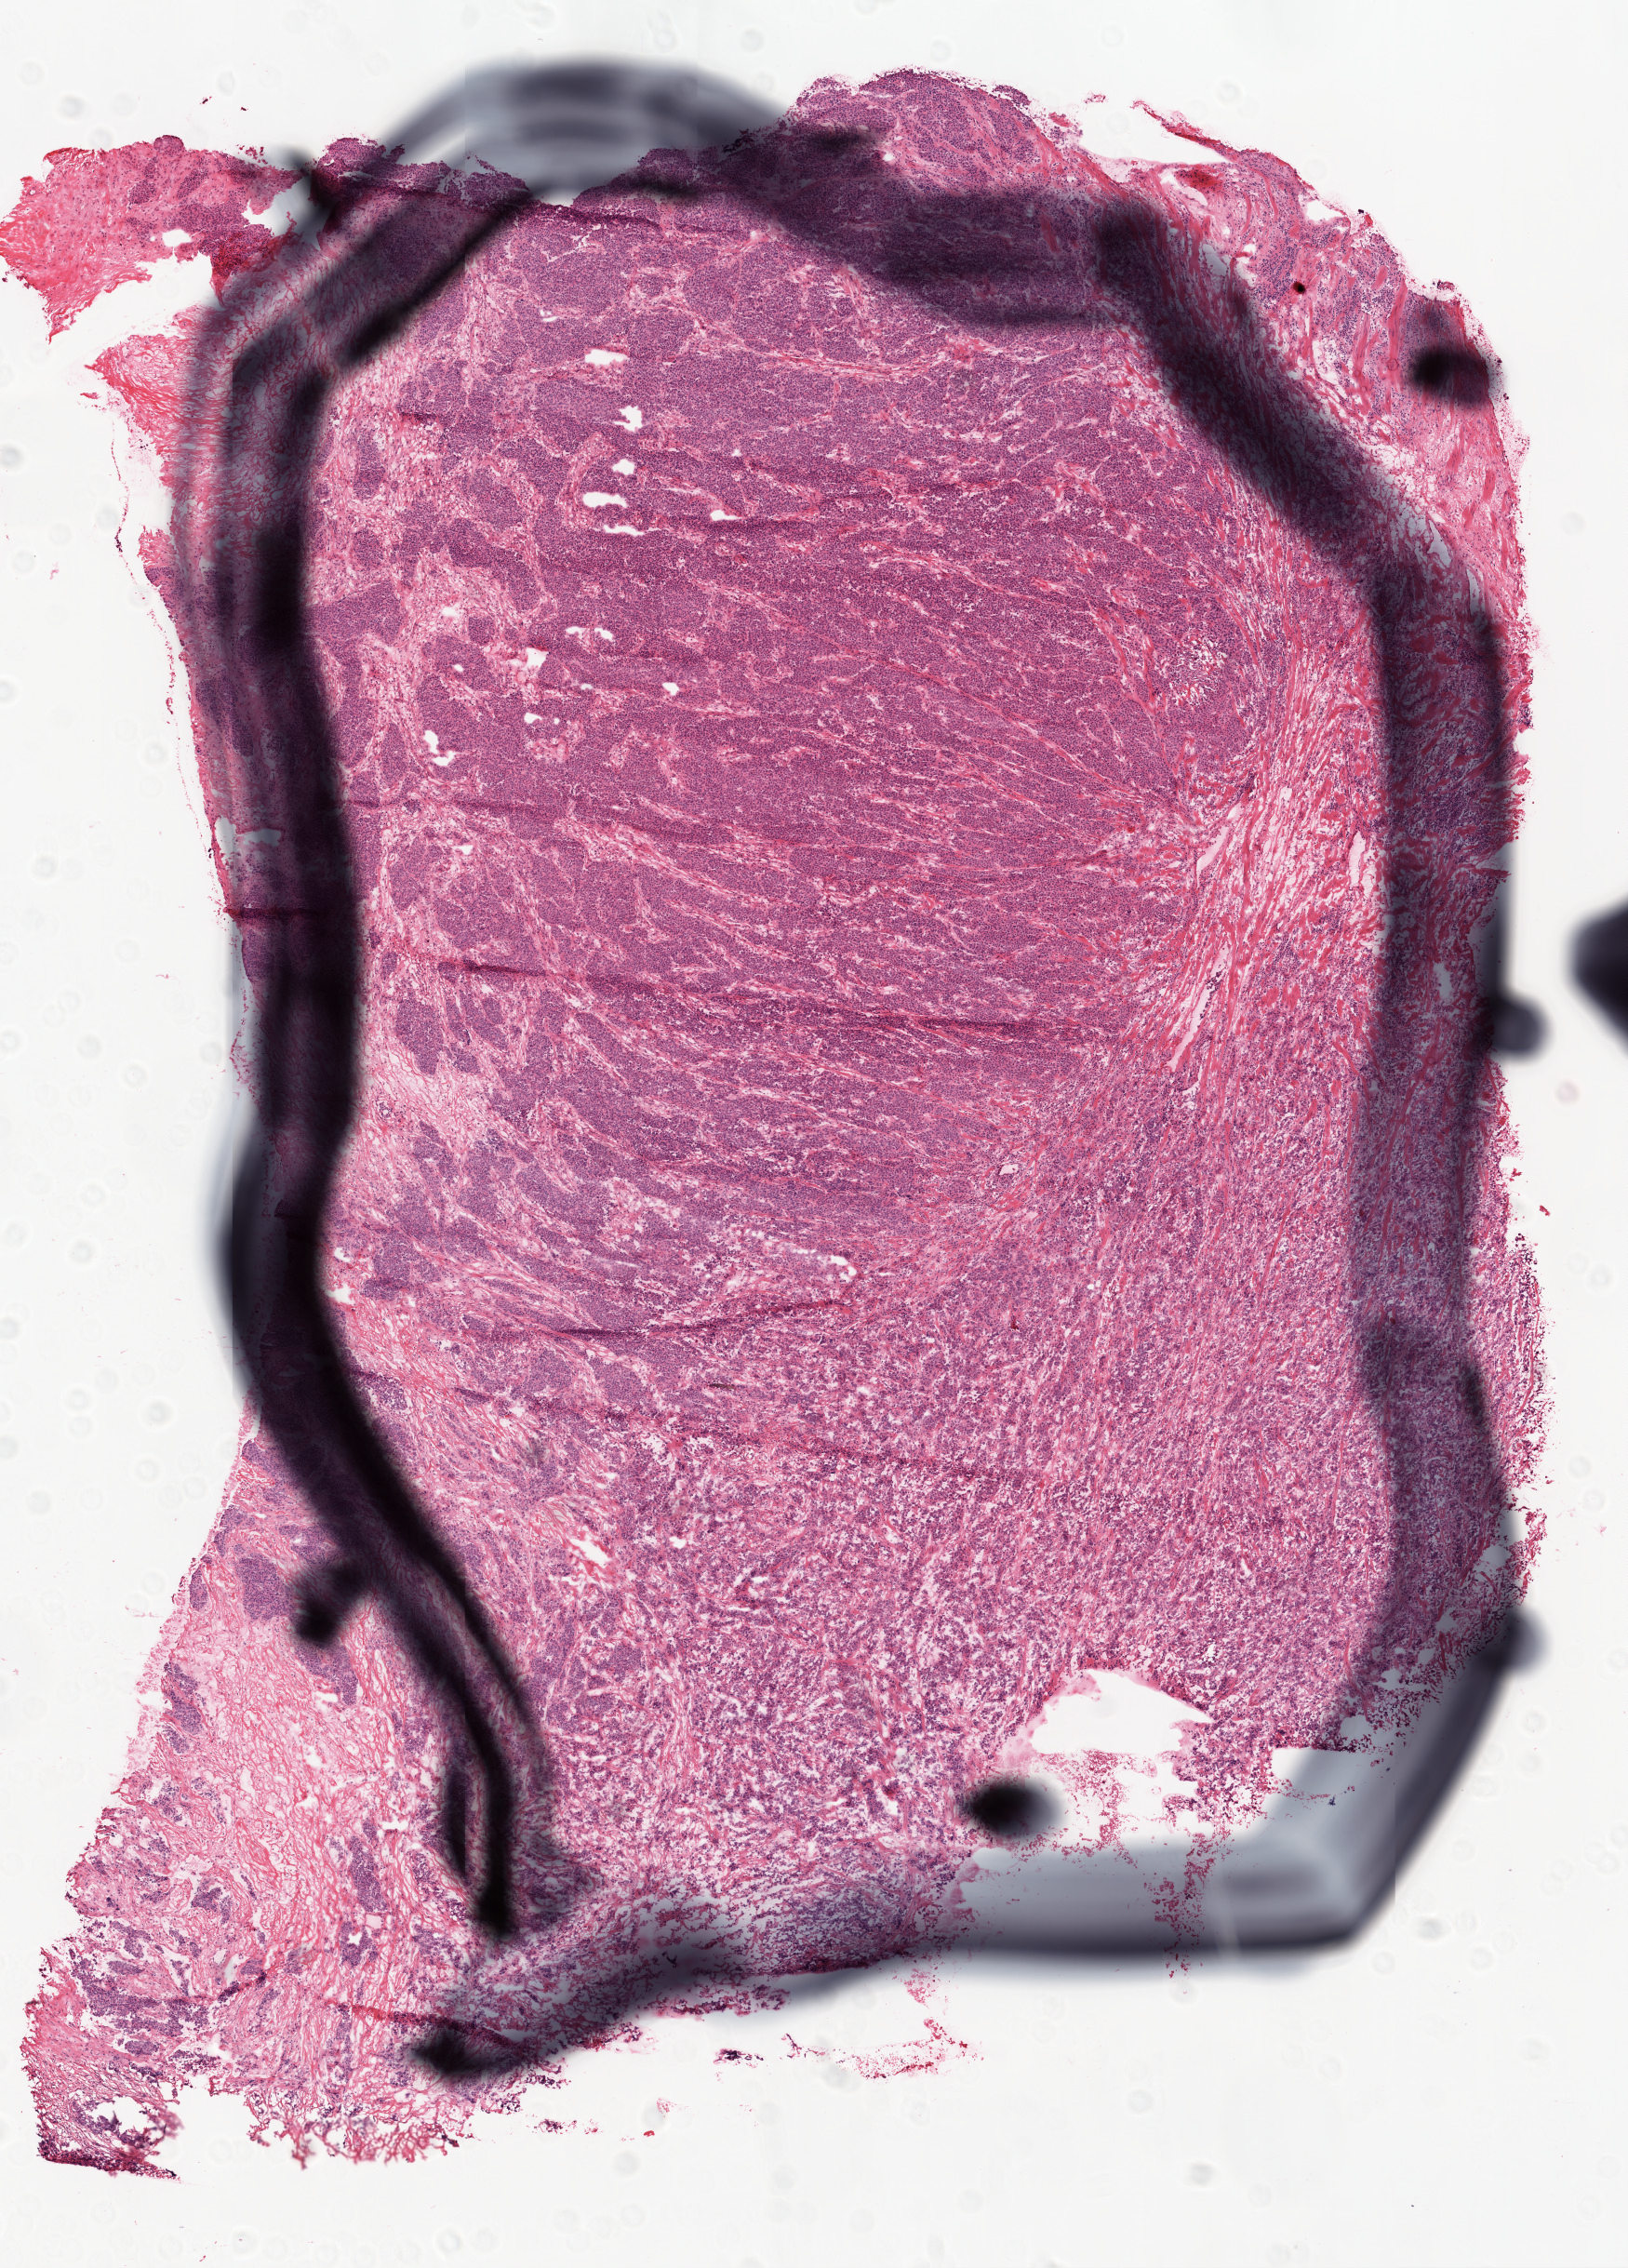
Digitized H&E-stained tissue section (whole slide), shown as a low-resolution overview of the whole scanned area (about 7.0 x 9.8 mm, slide scanned at 20x); frozen section from the top of the tissue portion; ovary, primary tumour sample. Female patient; age at initial diagnosis 71 years. Histologic grade: G3 (poorly differentiated). Slide review estimates, as recorded: tumour cells 98%, tumour nuclei 85%, normal cells 0%, stromal cells 0%, necrosis 2%. Inflammatory infiltration, as recorded: lymphocyte infiltration 10%.
Pathologic diagnosis: Serous cystadenocarcinoma, NOS. FIGO stage: IIIC. Laterality: right.